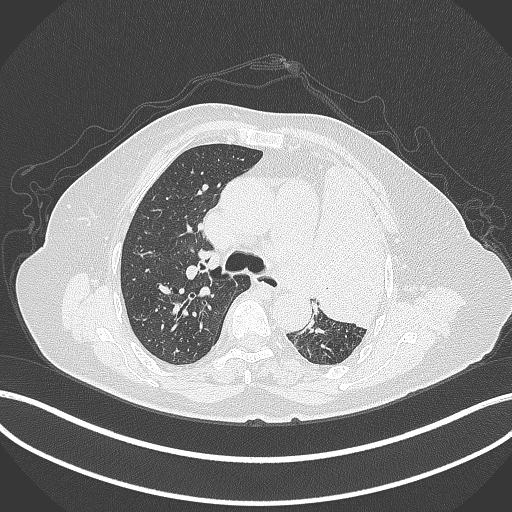
Chest CT, one axial slice; position 256 of 399 along the scan axis; reconstruction kernel B70f; 120 kVp; lung window (W 1500 / L -600 HU); 512 × 512 image matrix. Female patient, age 75 years. From the clinical record (not read from this slice): clinical TNM (as recorded): T3 N3 M1.
Annotated regions visible in this slice (rectangle marked by the reading radiologist):
- lung tumour (recorded histology: adenocarcinoma): box from (x=314, y=148) to (x=389, y=329) px